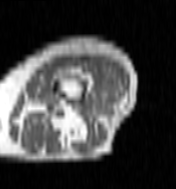
MRI of an extremity soft-tissue mass, one axial slice. Position 26 of 100 along the scan axis. MR volume resampled by the dataset authors to the PET/CT grid (not the native acquisition matrix). 3.27 mm slice thickness. 176 × 189 image matrix. Female patient. From the clinical record (not read from this slice): histological type: undifferentiated – high grade; grade: high; site of the primary tumour: left thigh.
Outlined on this slice (expert contour drawn on MRI and transferred to this co-registered scan by the dataset authors):
- gross tumour volume including surrounding oedema: bounding box [x1, y1, x2, y2] px = [69, 61, 118, 104]